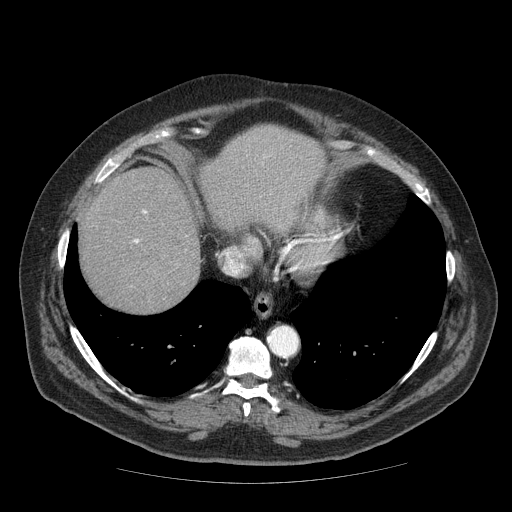
Contrast-enhanced abdominal CT (liver protocol), one axial slice. Position 61 of 85 along the scan axis. Reconstruction kernel STANDARD. 120 kVp. Soft-tissue window (W 400 / L 40 HU). 2.5 mm slice thickness. 512 × 512 image matrix. From the clinical record (not read from this slice): diagnosis: hepatocellular carcinoma (patient treated with transarterial chemoembolisation; whether this scan precedes or follows treatment is not stated here); TNM stage (as recorded): Stage-IIIA; Child-Pugh class: A; tumour nodularity: multinodular; tumour size: 7 cm.
Outlined on this slice (semi-automatically segmented with operator editing):
- abdominal aorta: bounding box (x1, y1, x2, y2) in pixels: (268, 327, 297, 356)
- liver parenchyma outside the tumour (the mass and vessels are separate outlines, so this box may not span the whole liver): (80, 126, 324, 312)
- liver vessels: (135, 211, 146, 243)